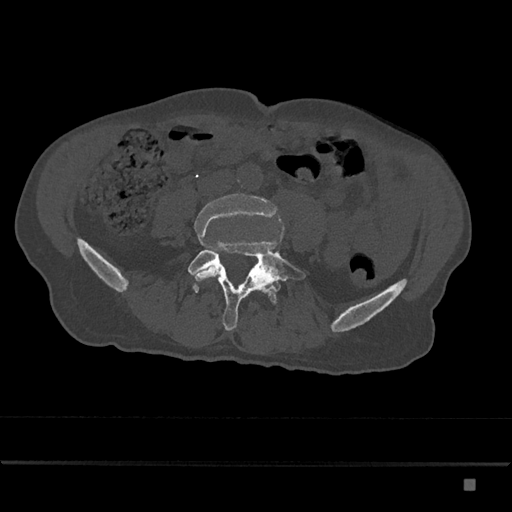
CT including the spine, one axial slice. Slice 297 of 797 in the series (ordered by position). Reconstruction kernel Br40s/3. 120 kVp. Bone window (W 1800 / L 400 HU). 0.5 mm slice thickness. 512 × 512 image matrix. Patient: male, 72 years. Case-level facts recorded for this patient, not image findings: primary cancer: prostate.
Outlined on this slice (semi-automatic segmentation, software-assisted and operator-edited):
- L4 vertebra: bounding box [x1, y1, x2, y2] px = [193, 193, 279, 281]
- L5 vertebra: [188, 241, 306, 331]